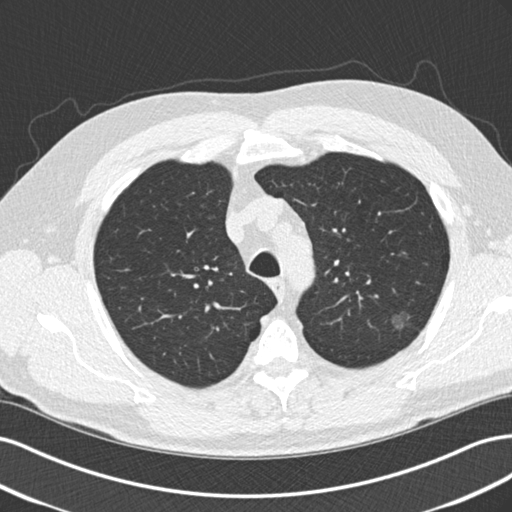
Low-dose screening chest CT, one axial slice. Position 165 of 209 along the scan axis. Reconstruction kernel B30f. 120 kVp. Lung window (W 1500 / L -600 HU). 2 mm slice thickness. 512 × 512 image matrix, field of view 360 × 360 mm.
Annotated regions visible in this slice (expert manual segmentation):
- lesion 1 (tumor, upper lobe of left lung): bounding box <392,315,404,329> (left, top, right, bottom; pixels)